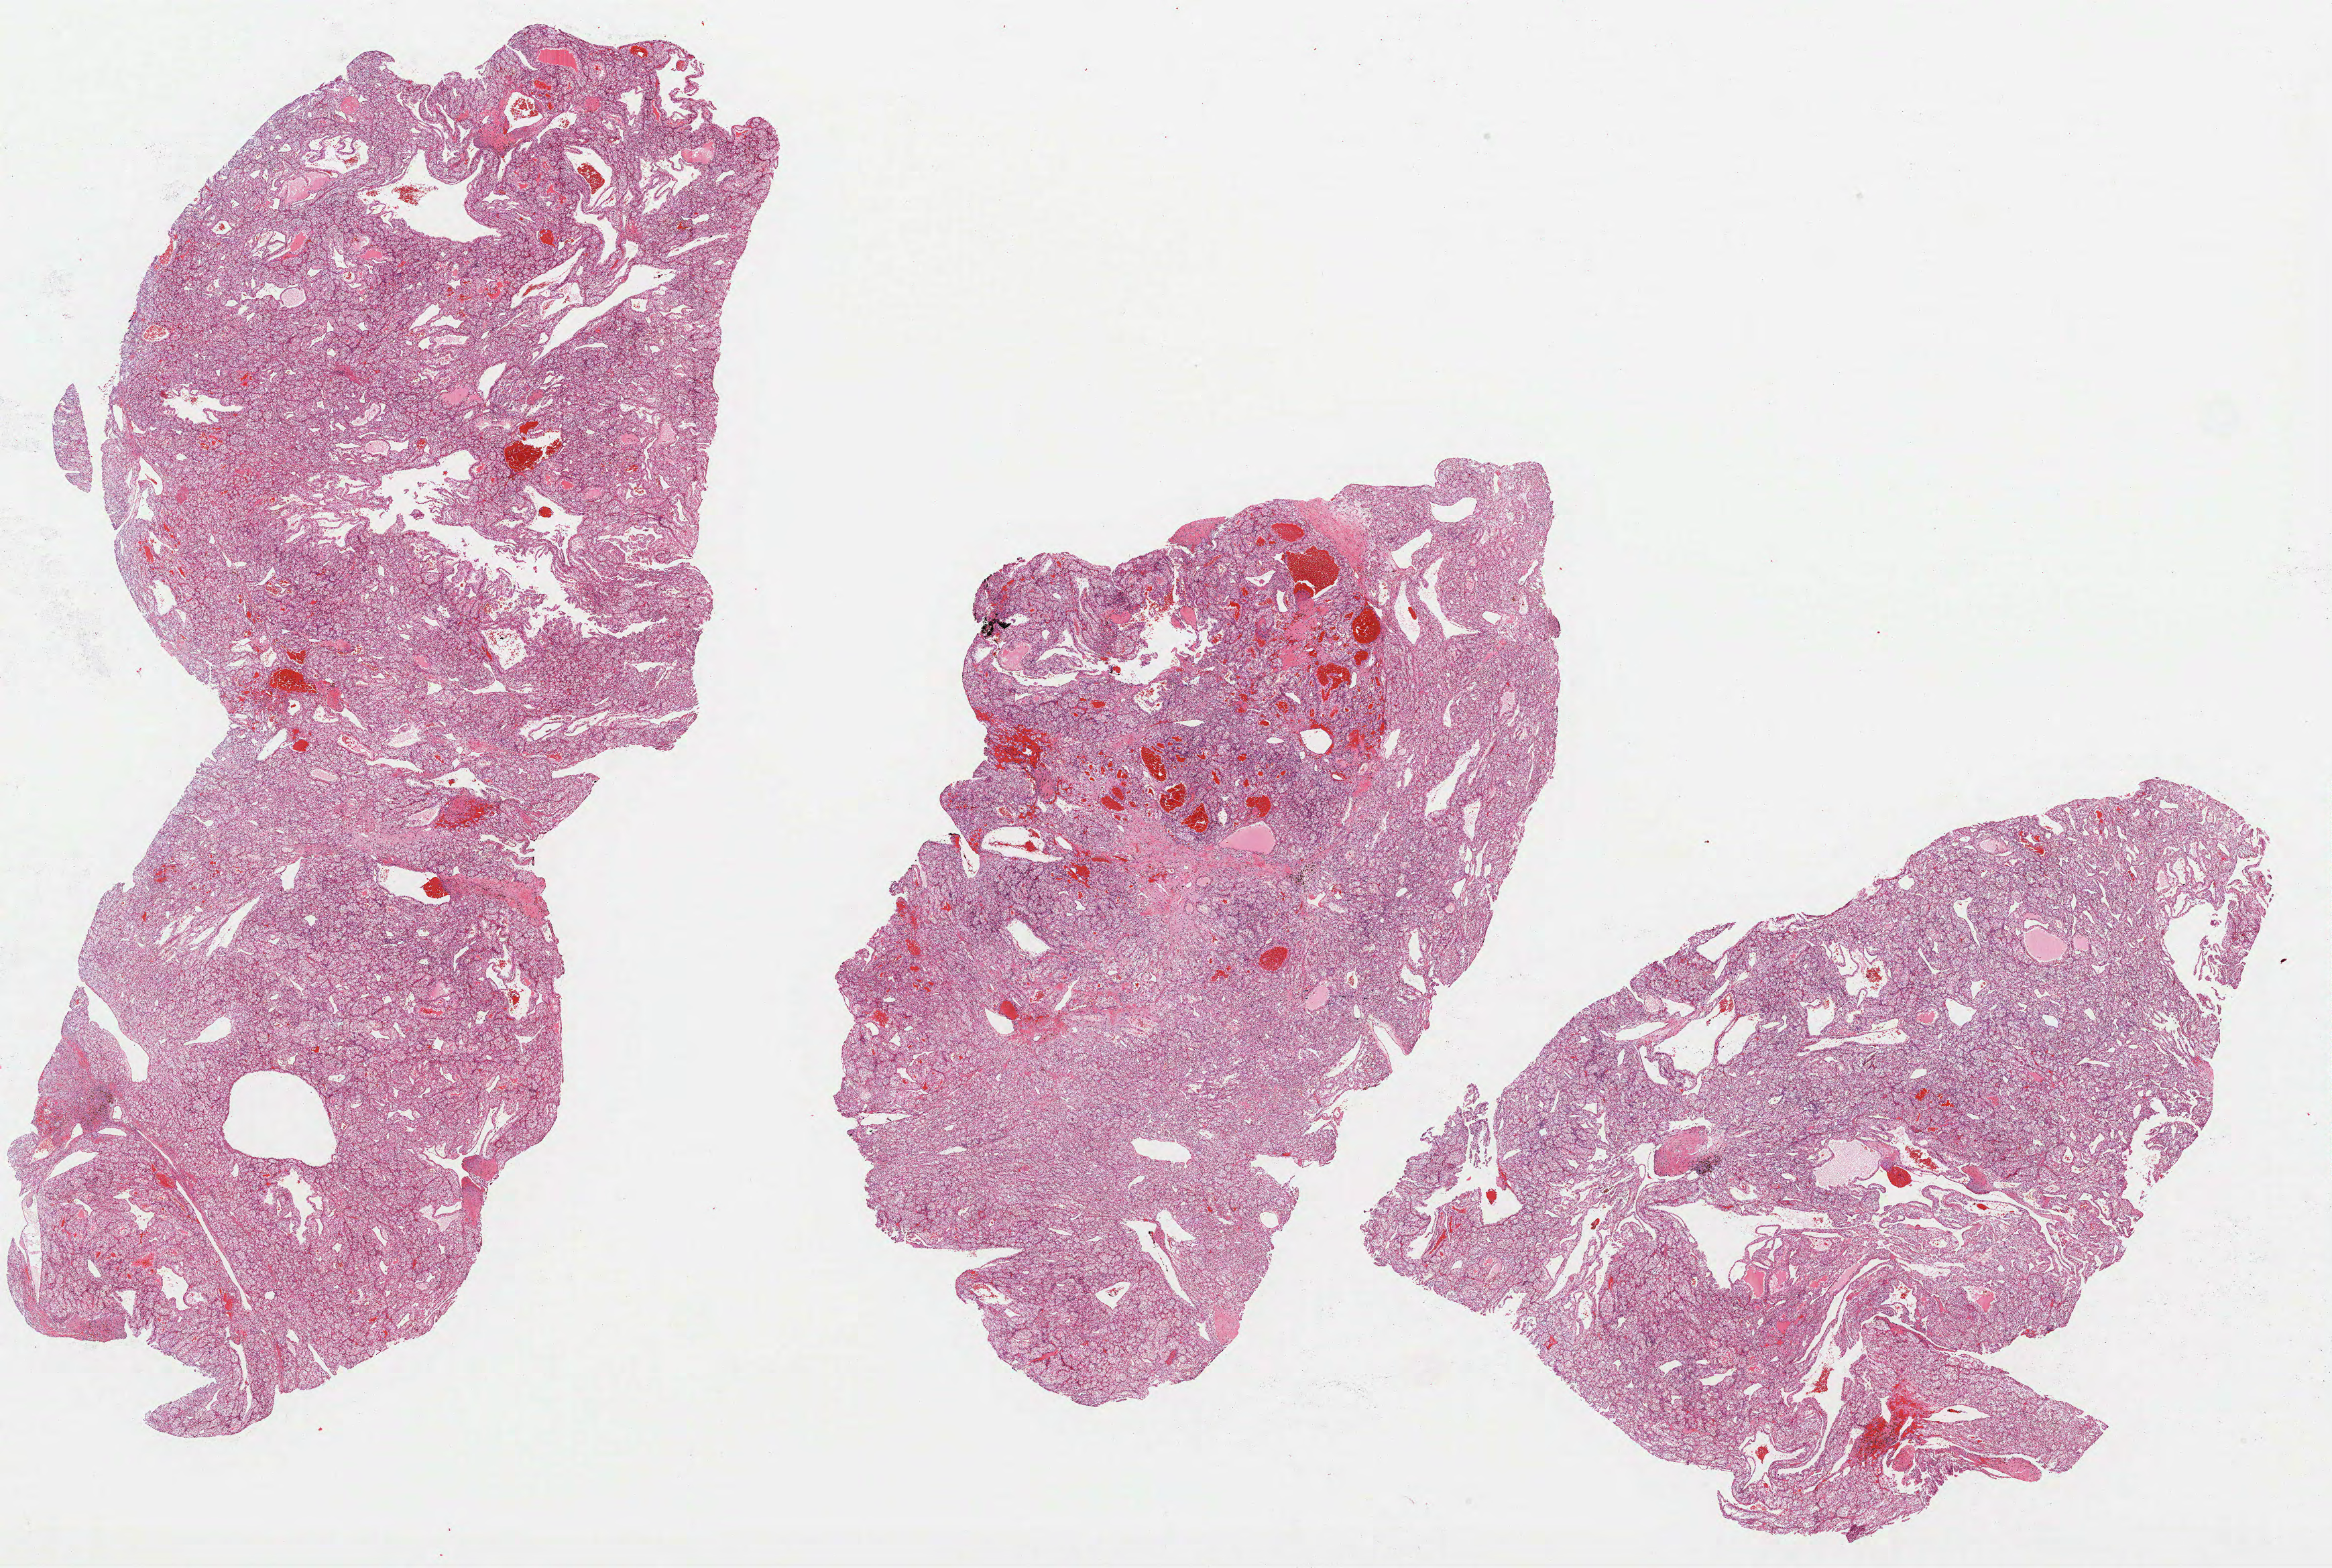
Whole-slide histology image, H&E-stained — a low-resolution overview of the entire scanned area, about 28.0 x 18.9 mm (slide scanned at 40x); formalin-fixed paraffin-embedded (FFPE) diagnostic section; kidney, primary tumour sample. Male patient; age at initial diagnosis 61 years. Histologic grade: G3 (poorly differentiated).
• lymph nodes positive (case pathology): 0 of 4 examined
• AJCC pathologic stage: I
• pathologic diagnosis: Clear cell adenocarcinoma, NOS